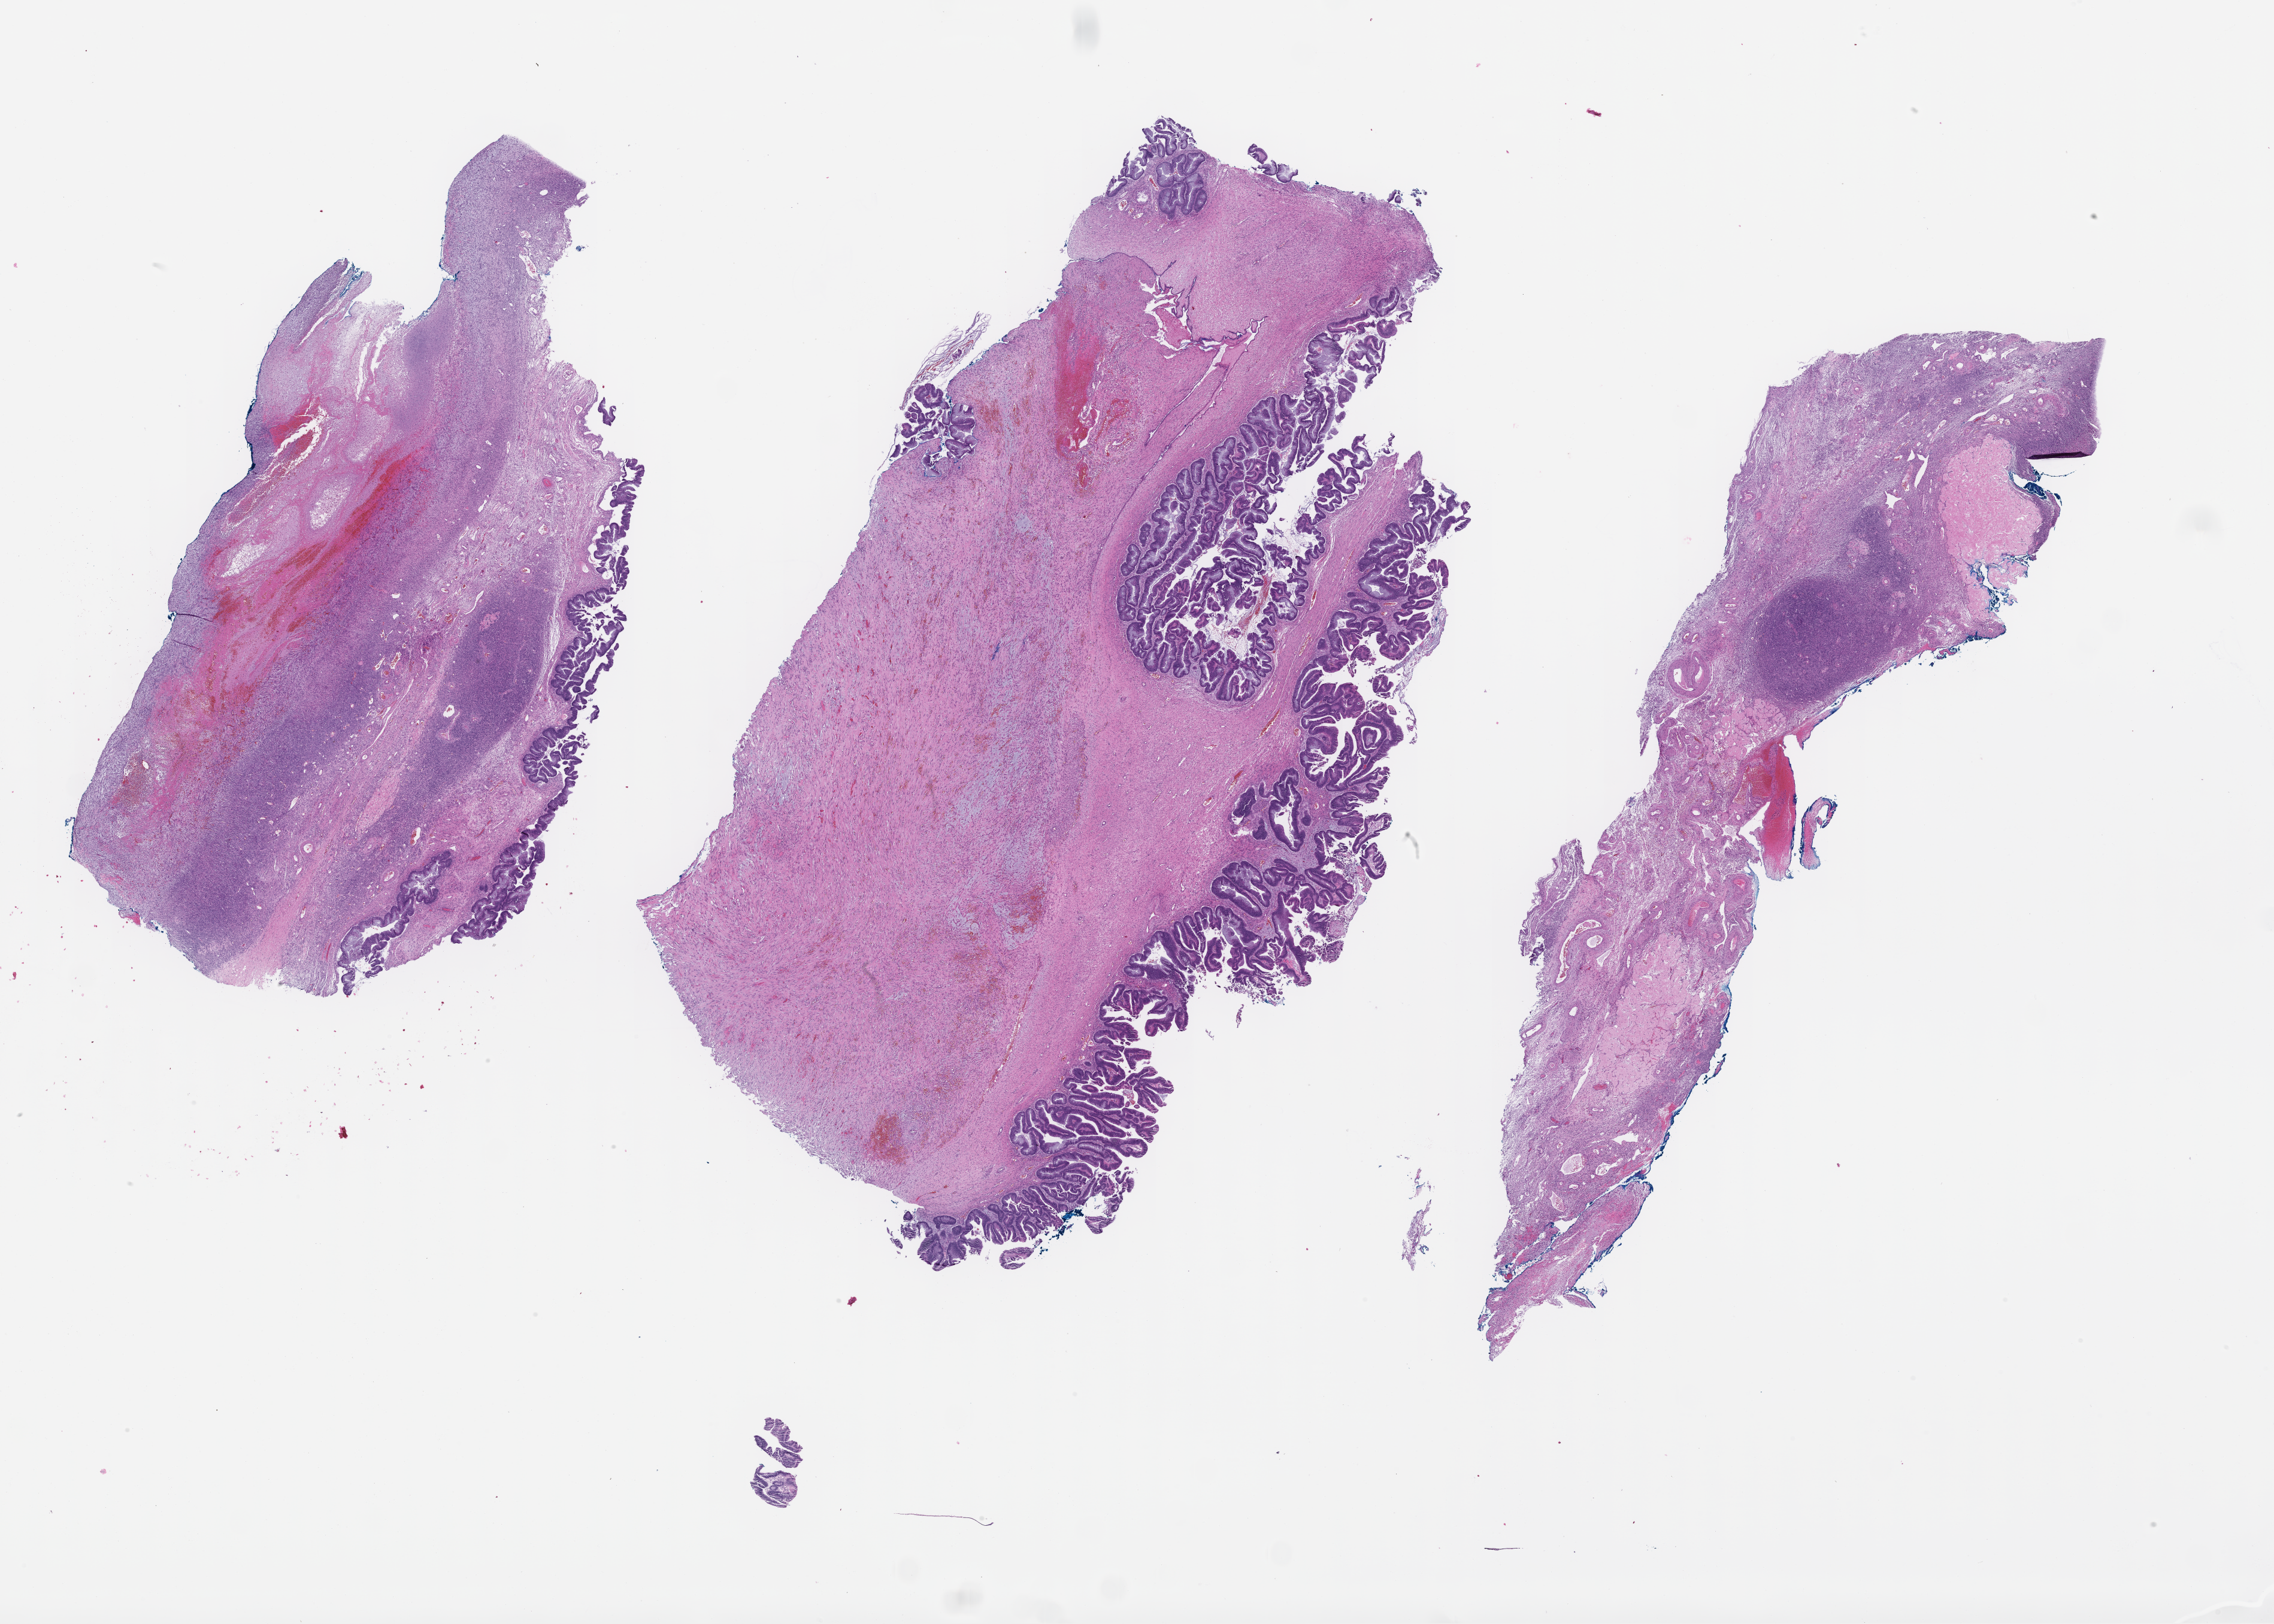
Haematoxylin and eosin whole-slide image — a low-resolution overview of the entire scanned area, about 30.7 x 21.9 mm. Formalin-fixed, paraffin-embedded (FFPE) tissue. Patient sex: female.
- this section: metastasis (sampled organ not recorded)
- primary diagnosis of the patient: Colorectal Carcinoma